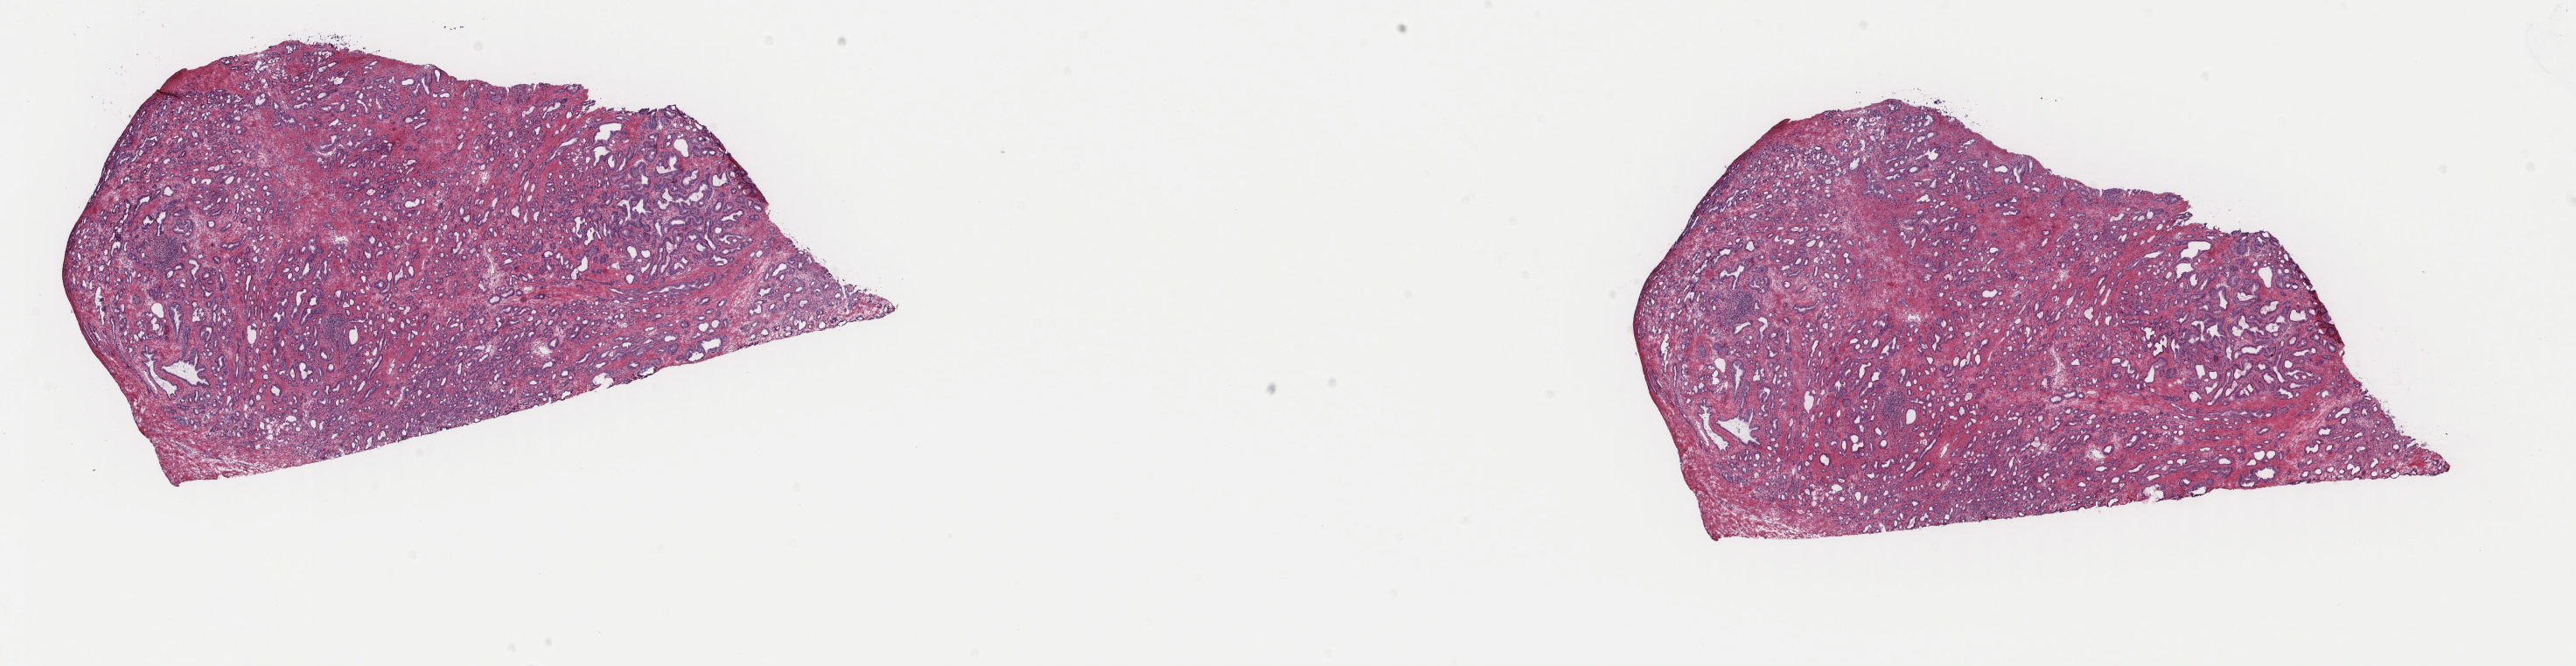
Hematoxylin and eosin (H&E) stained whole-slide image, a low-resolution overview of the entire scanned area, about 23.4 x 6.0 mm (acquisition: 40x scan). Frozen section from the top of the tissue portion. Primary tumour sample from the prostate. Male, age 69 years at initial diagnosis. Gleason score: 7 (3+4). Composition of this section per pathologist review: tumour cells 45%, tumour nuclei 85%, normal cells 2%, stromal cells 53%, necrosis 0%. Infiltration values recorded for this section: lymphocyte infiltration 6%, monocyte infiltration 0%, neutrophil infiltration 0%.
Lymph nodes positive (case pathology): 0 of 4 examined. Pathologic diagnosis: Adenocarcinoma, NOS.